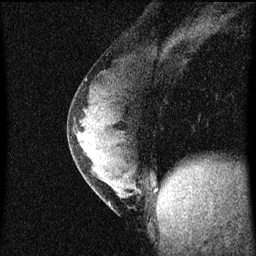
Breast MRI (dynamic contrast-enhanced), one sagittal slice; slice 27 of 60 in the series (ordered by position); dynamic contrast-enhanced series, image 2 of 4 at this slice position (ordered by acquisition); 1.5 T; TE 4.2 ms, TR 8 ms; 2 mm slice thickness; 256 × 256 image matrix. Patient: female, 33 years.
Annotated regions visible in this slice (semi-automatic segmentation, software-assisted and operator-edited):
- analysis volume of interest (the breast-tissue region the enhancement analysis was run in; not a lesion): box from (x=68, y=76) to (x=149, y=215) px
- tumour enhancement mask (voxels above the 70 % enhancement threshold inside the analysis volume of interest): (x=77, y=124)–(x=110, y=205)